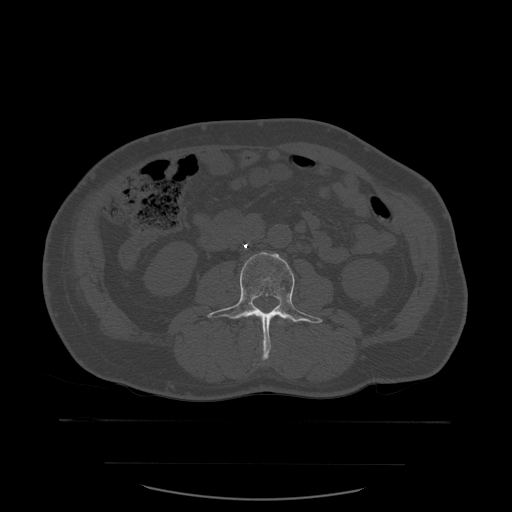
CT including the spine, one axial slice. Slice 195 of 590 in the series (ordered by position). Bone window (W 1800 / L 400 HU). 1.25 mm slice thickness. 512 × 512 image matrix. Patient age 71 years. From the clinical record (not read from this slice): primary cancer: lung; vertebrae with lytic lesions (as recorded): T1, T2, L5, S1.
Annotated regions visible in this slice (semi-automatically segmented with operator editing):
- L2 vertebra: bounding box <261,318,283,360> (left, top, right, bottom; pixels)
- L3 vertebra: <207,252,323,359>